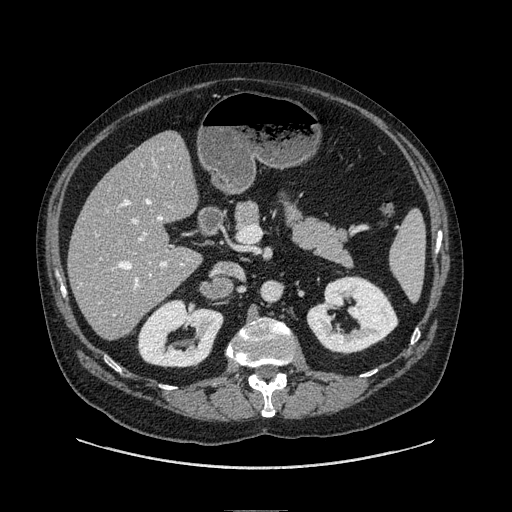
Contrast-enhanced abdominal CT, one axial slice; slice 33 of 149 in the series (ordered by position); soft-tissue window (W 400 / L 40 HU); 512 × 512 image matrix, field of view 440 × 440 mm. Male patient. Case-level facts recorded for this patient, not image findings: diagnosis: adrenocortical carcinoma; tumour side: right adrenal.
Structures marked on this image (semi-automatic segmentation, software-assisted and operator-edited):
- mass: bounding box <203,281,228,297> (left, top, right, bottom; pixels)